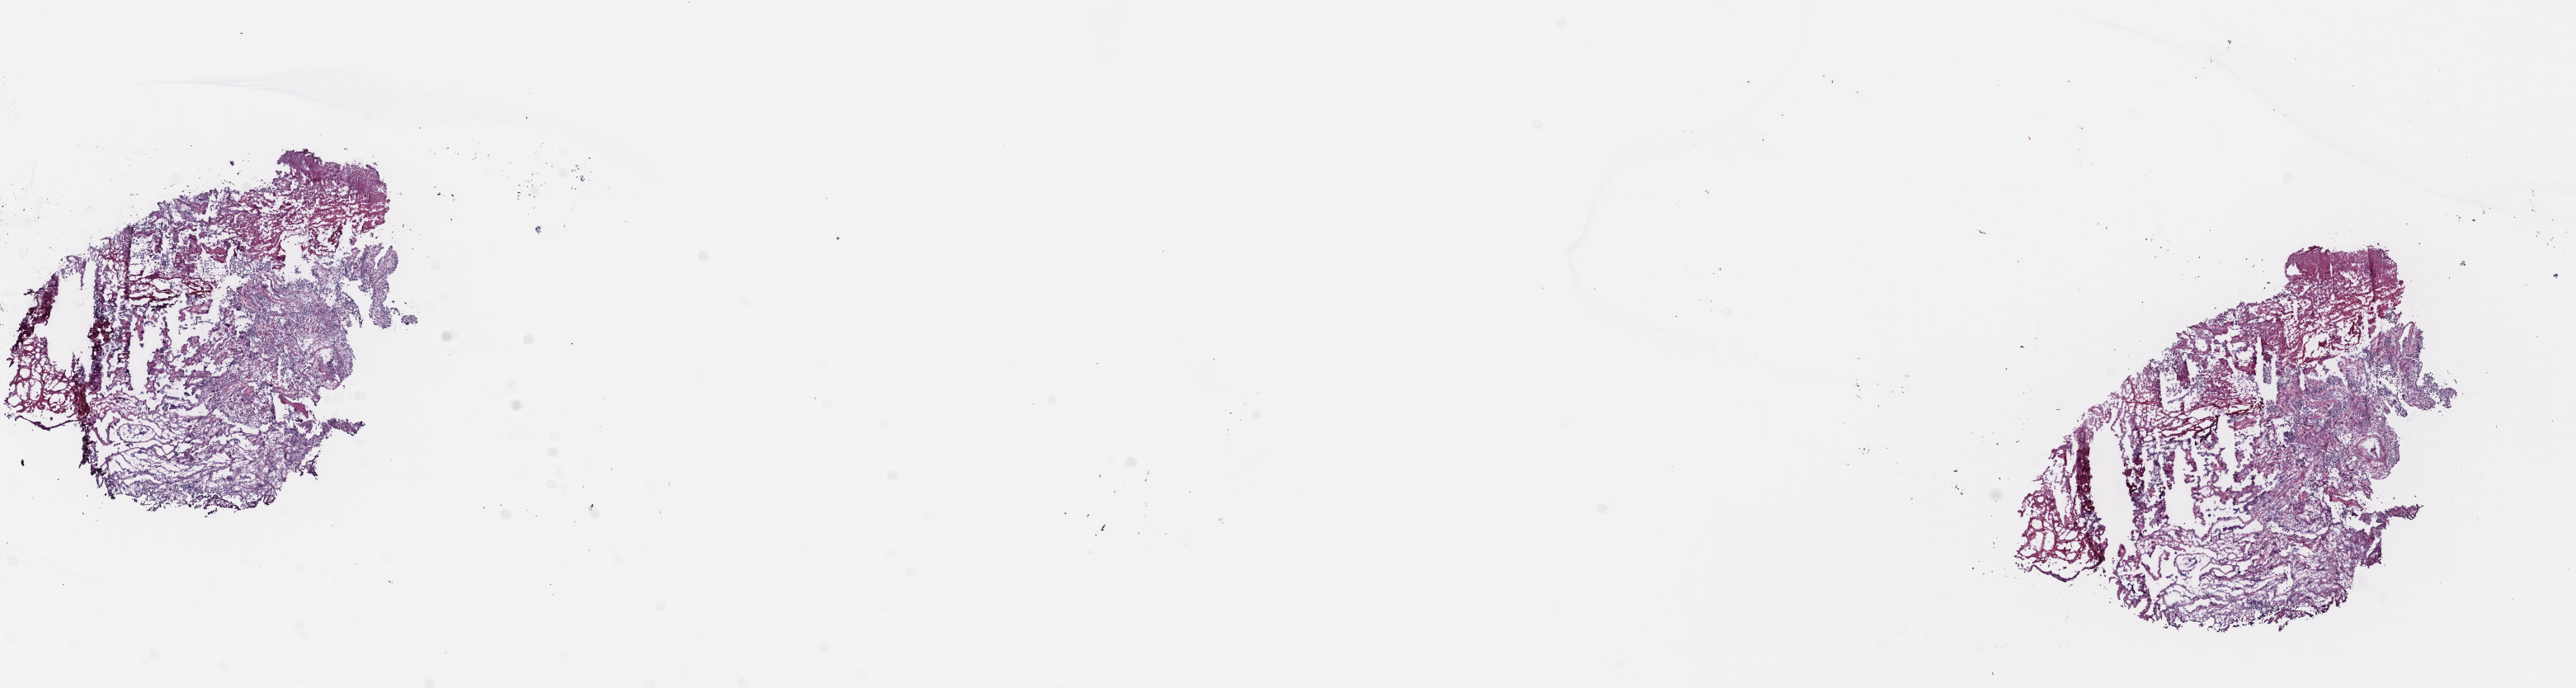
Whole-slide histology image, H&E — whole scanned area (about 24.6 x 6.6 mm, acquisition: 40x scan) shown as a low-resolution overview. Frozen section from the top of the tissue portion. Primary tumour sample from the bladder. Male patient; age at initial diagnosis 68 years. Histologic grade: high grade. Slide review estimates, as recorded: tumour cells 70%, tumour nuclei 80%, normal cells 0%, stromal cells 20%, necrosis 10%. Infiltration values recorded for this section: lymphocyte infiltration 0%, monocyte infiltration 0%, neutrophil infiltration 0%.
AJCC pathologic stage: IV (7th edition). Lymph nodes positive (case pathology): 2 of 10 examined. Histologic diagnosis: Transitional cell carcinoma. TNM: T4a N2 MX.